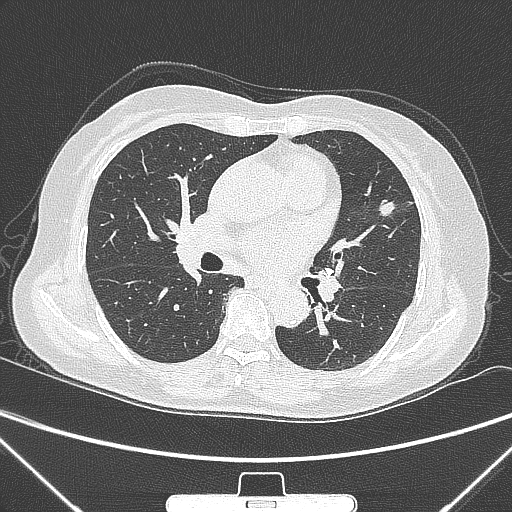
Chest CT, one axial slice. Position 149 of 300 along the scan axis. 120 kVp. Lung window (W 1500 / L -600 HU). 1 mm slice thickness. 512 × 512 image matrix, field of view 350 × 350 mm. Patient: female, 70 years. From the clinical record (not read from this slice): clinical TNM (as recorded): T1b N0 M0.
Outlined on this slice (rectangle marked by the reading radiologist):
- lung tumour (recorded histology: adenocarcinoma): bounding box [x1, y1, x2, y2] px = [375, 194, 402, 226]